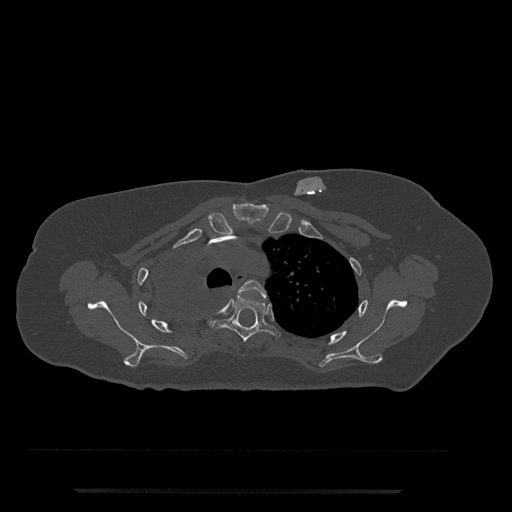
CT including the spine, one axial slice; position 597 of 797 along the scan axis; 120 kVp; bone window (W 1800 / L 400 HU); 0.5 mm slice thickness; 512 × 512 image matrix, field of view 440 × 440 mm. Female patient, age 51 years. From the clinical record (not read from this slice): primary cancer: neuro.
Annotated regions visible in this slice (semi-automatically segmented with operator editing):
- T3 vertebra: bounding box [x1, y1, x2, y2] px = [238, 280, 267, 299]
- T4 vertebra: [210, 297, 281, 342]